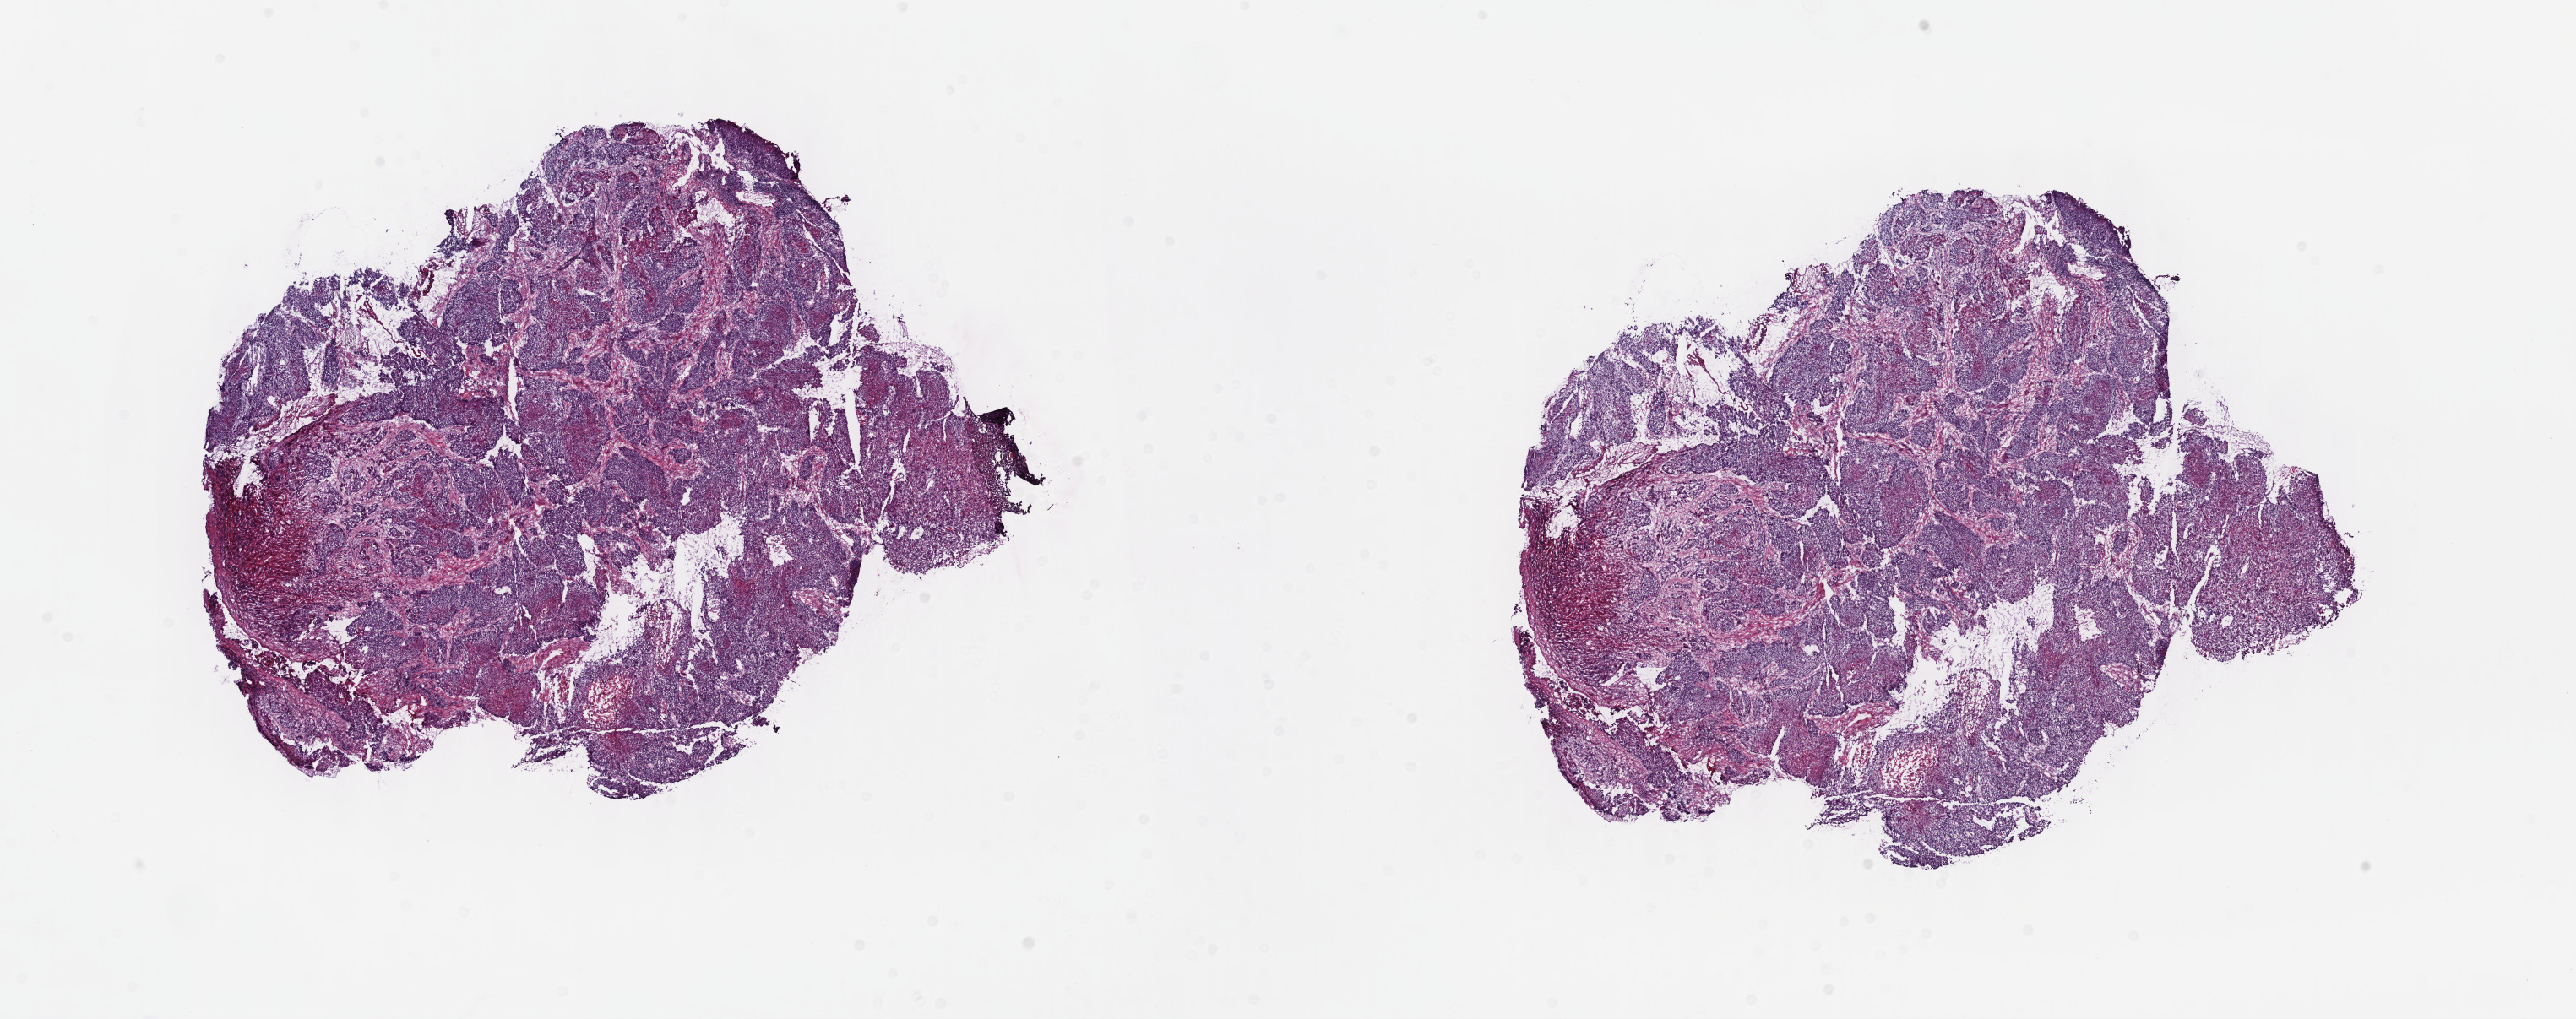
Digitized H&E-stained tissue section (whole slide), low-resolution overview of the scanned area, about 24.7 x 9.8 mm (from a 40x scan), frozen section, sample: primary tumour, cervix. Female, age 56 years at initial diagnosis. Histologic grade: G2 (moderately differentiated). Slide review estimates, as recorded: tumour cells 85%, tumour nuclei 85%, normal cells 0%, stromal cells 15%, necrosis 0%. Infiltration values recorded for this section: lymphocyte infiltration 5%, monocyte infiltration 0%, neutrophil infiltration 0%.
FIGO stage: IIIB. Diagnosis: Squamous cell carcinoma, NOS (cervix uteri).